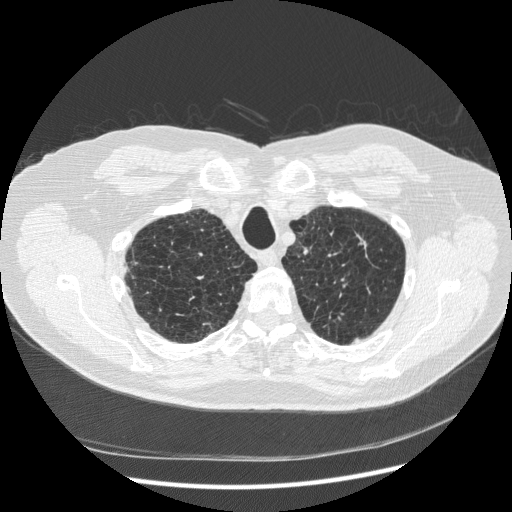
Chest CT (low-dose screening protocol), one axial image, baseline screening round, lung window (W 1500 / L -600 HU), standard (soft-tissue) reconstruction kernel (STANDARD), slice 43 of 265 in the series, 512 × 512 image matrix, field of view 380 × 380 mm. Male, age 70 years at enrolment. Former smoker at enrolment.
- Lesion marked by an expert reader, bounding box [x1, y1, x2, y2] px = [332, 217, 387, 272].
- The screening reader recorded 2 non-calcified nodules or masses ≥4 mm on this exam; which of them this box marks is not recorded.